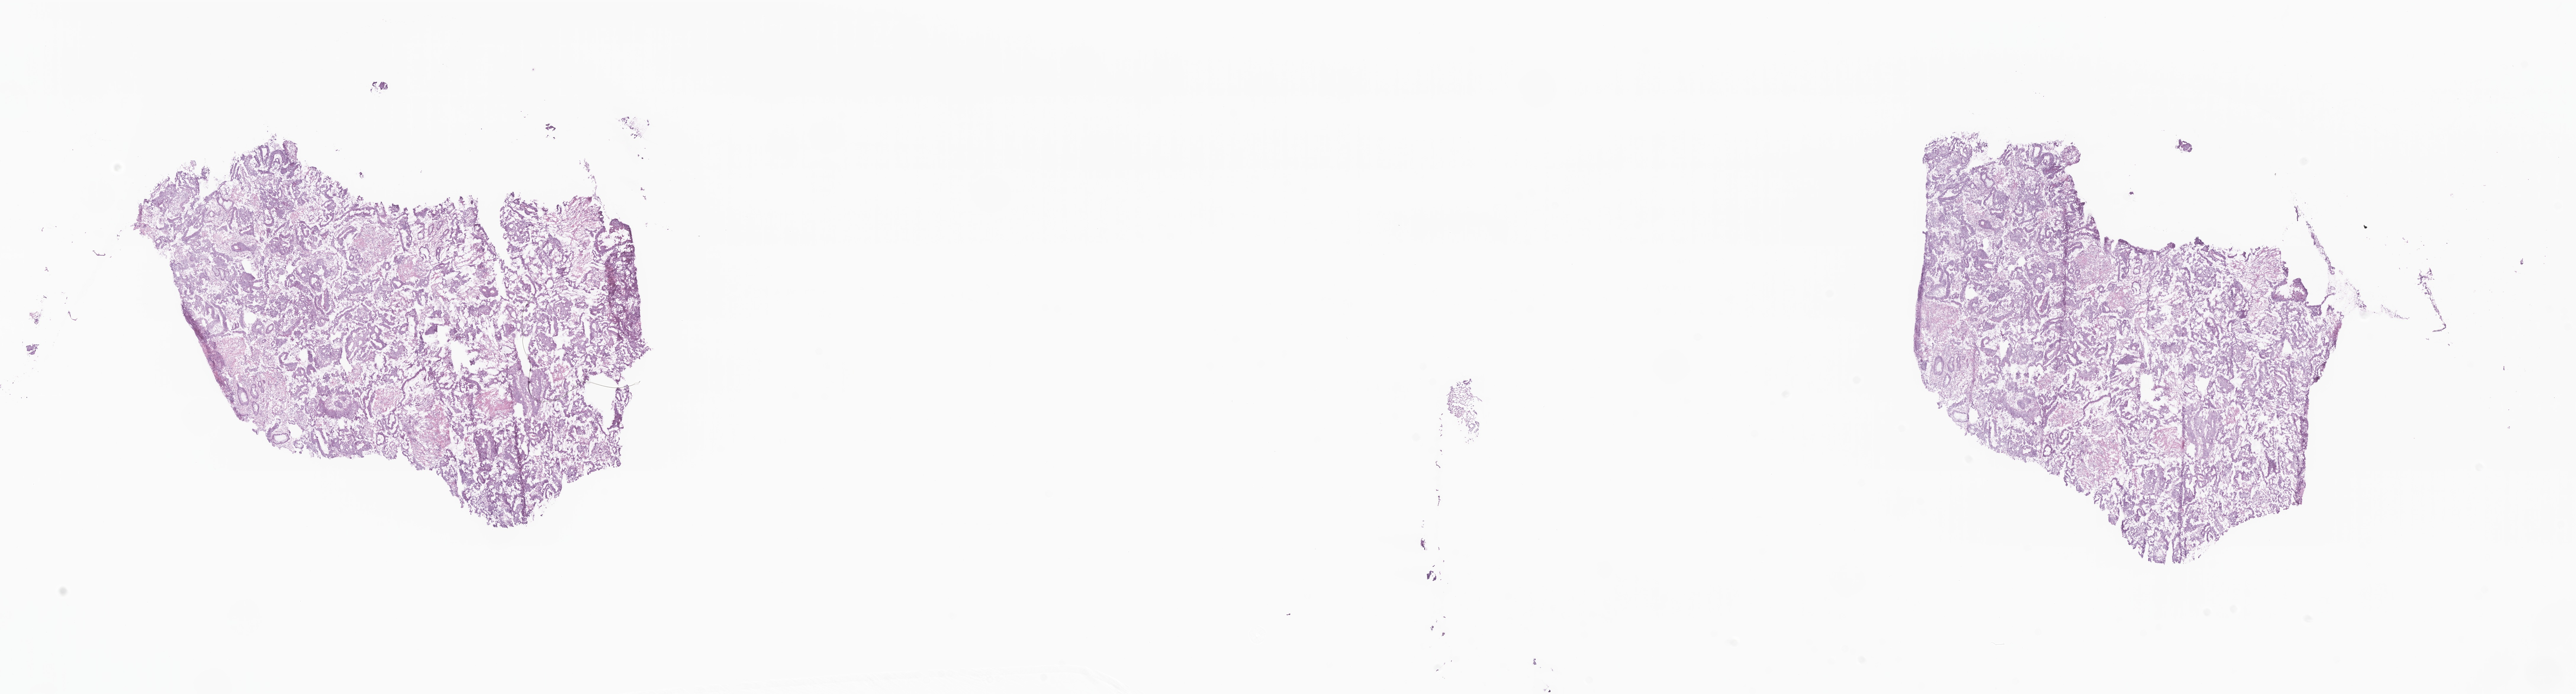
H&E whole-slide image, shown as a low-resolution overview of the whole scanned area (about 36.7 x 9.9 mm); frozen section (tissue freezing medium); specimen: primary tumor; anatomic site: sigmoid colon. Female patient; age at initial diagnosis 62 years. Tumor grade: G1 (well differentiated). Composition of this section per pathologist review: tumor cells 49%, tumor nuclei 70%, stromal cells 48%, necrosis 2%, normal cells 1%. Inflammatory infiltration, as recorded: lymphocyte infiltration 22%, monocyte infiltration 2%, neutrophil infiltration 0%.
* AJCC pathologic stage: Stage IVB
* histologic diagnosis: Adenocarcinoma, NOS
* section: bottom of the tissue portion